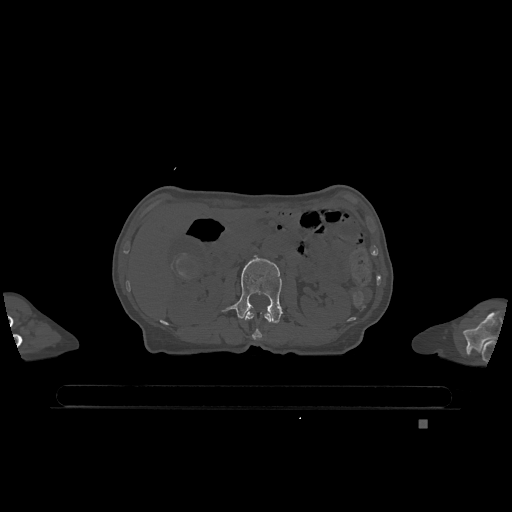
CT including the spine, one axial slice; slice 430 of 1317 in the series (ordered by position); bone window (W 1800 / L 400 HU); 512 × 512 image matrix. Patient: female, 74 years. From the clinical record (not read from this slice): primary cancer: lung; vertebrae with lytic lesions (as recorded): T1, T4, T5, T6, L4, L5.
Structures marked on this image (semi-automatically segmented with operator editing):
- L1 vertebra: bounding box (x1, y1, x2, y2) in pixels: (244, 311, 272, 340)
- L2 vertebra: (223, 257, 282, 323)